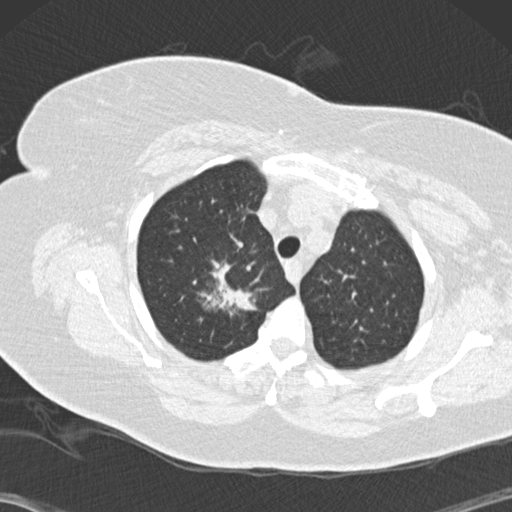
Low-dose screening chest CT, one axial slice. Slice 118 of 146 in the series (ordered by position). Reconstruction kernel B30f. Lung window (W 1500 / L -600 HU). 512 × 512 image matrix, field of view 350 × 350 mm.
Outlined on this slice (manually delineated by an expert):
- lesion 1 (tumor, upper lobe of right lung): bounding box <200,264,256,310> (left, top, right, bottom; pixels)